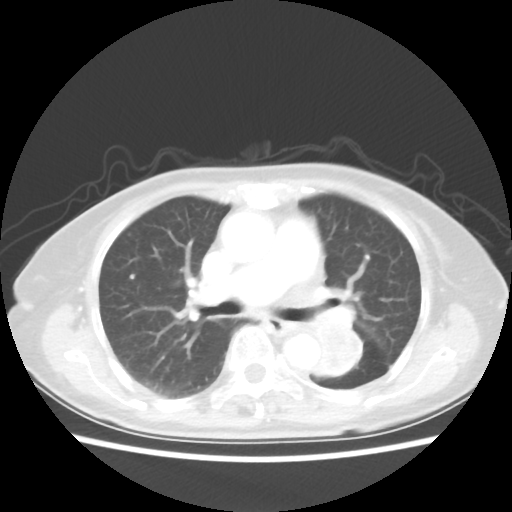
Chest CT, one axial slice; slice 30 of 50 in the series (ordered by position); reconstruction kernel STANDARD; lung window (W 1500 / L -600 HU); 5 mm slice thickness; 512 × 512 image matrix, field of view 335 × 335 mm. Female patient, age 81 years. From the clinical record (not read from this slice): clinical TNM (as recorded): T2 N0 M1a.
Annotated regions visible in this slice (bounding box drawn by a radiologist):
- lung tumour (recorded histology: squamous cell carcinoma): bounding box [x1, y1, x2, y2] px = [313, 321, 377, 385]